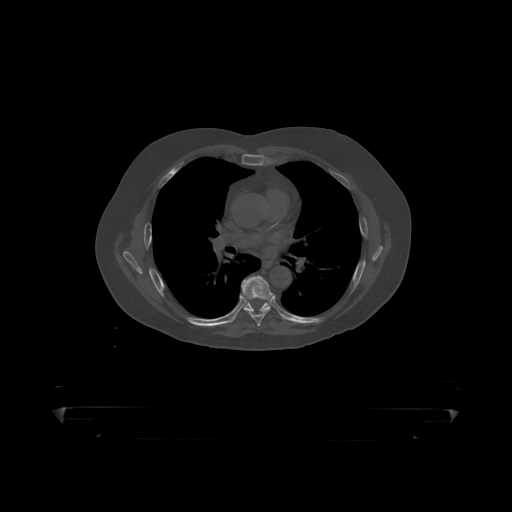
CT including the spine, one axial slice. Slice 291 of 390 in the series (ordered by position). Reconstruction kernel STANDARD. 120 kVp. Bone window (W 1800 / L 400 HU). 1.25 mm slice thickness. 512 × 512 image matrix, field of view 650 × 650 mm. Male patient, age 60 years. Case-level facts recorded for this patient, not image findings: primary cancer: prostate.
Annotated regions visible in this slice (semi-automatically segmented with operator editing):
- T6 vertebra: bounding box (x1, y1, x2, y2) in pixels: (242, 276, 273, 319)
- T7 vertebra: (244, 300, 271, 313)